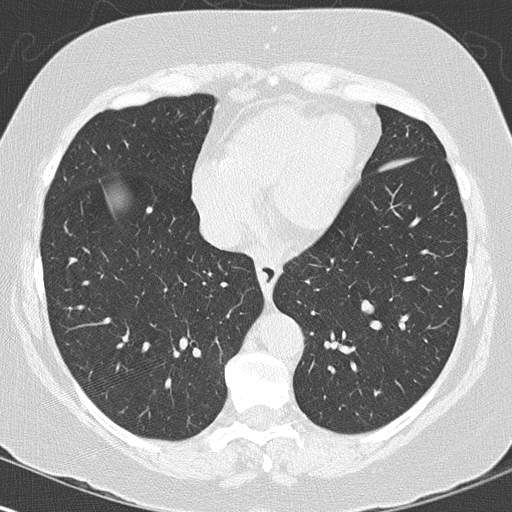
Axial slice from a low-dose chest CT screening exam. Baseline screening round. Lung window (W 1500 / L -600 HU). Lung (sharp) reconstruction kernel (B50f). Female, age 60 years at enrolment. Former smoker at enrolment.
- Lesion marked by an expert reader, bounding box [x1, y1, x2, y2] px = [347, 292, 388, 328].
- The exam's reader record, not a measurement of the box and not confirmed to be the same lesion: non-calcified nodule or mass ≥4 mm, left lower lobe, 12 × 10 mm, smooth margins, soft tissue attenuation.
- Official screen result: positive, change unspecified: nodule(s) >= 4 mm or enlarging nodule(s), mass(es), or other non-specific abnormalities suspicious for lung cancer.